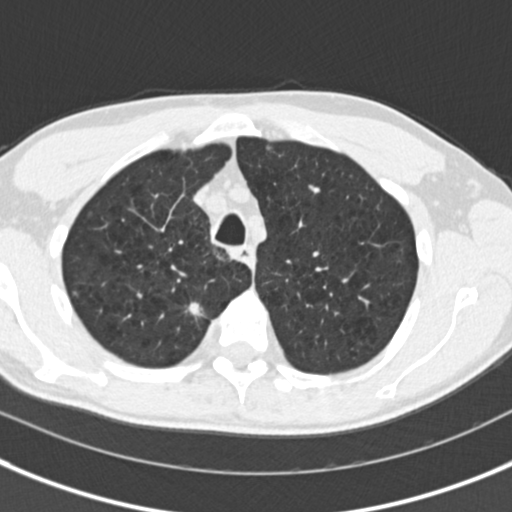
Low-dose screening chest CT, one axial slice; reconstruction kernel B30f; lung window (W 1500 / L -600 HU); 2 mm slice thickness; 512 × 512 image matrix.
Outlined on this slice (expert manual segmentation):
- lesion 2 (tumor, upper lobe of right lung): box from (x=186, y=302) to (x=204, y=317) px